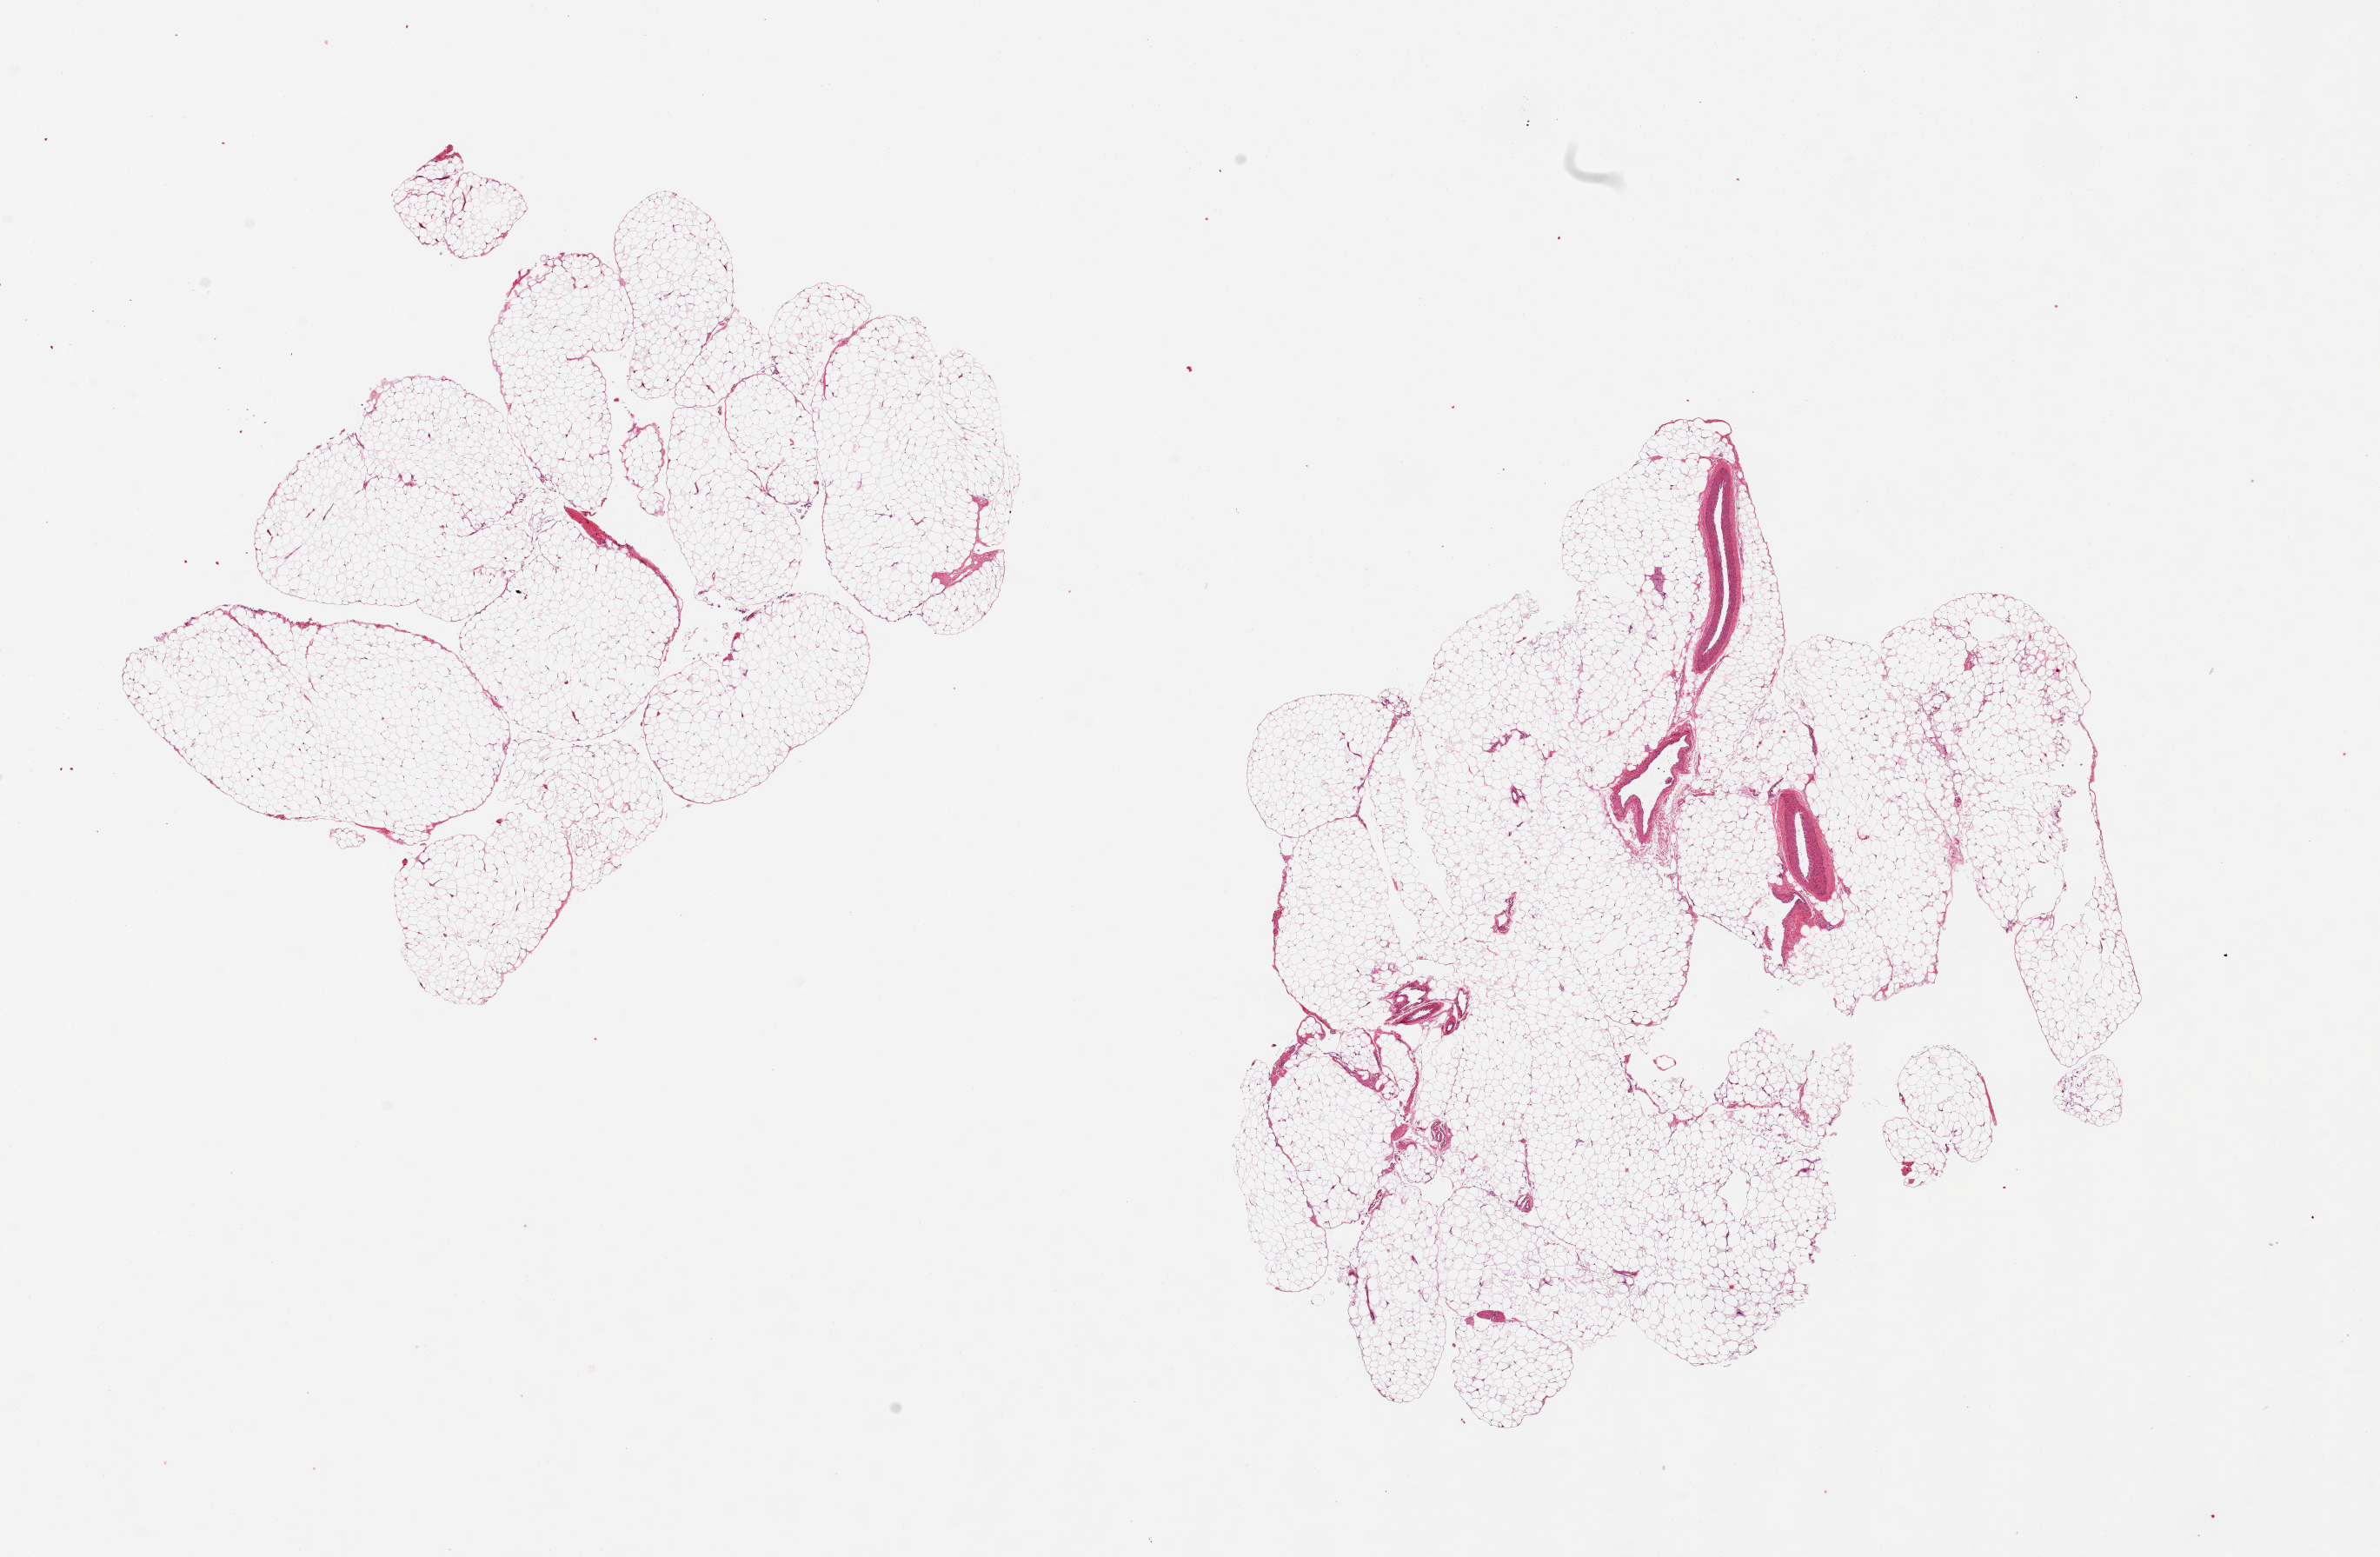
Whole-slide image, H&E stain, brightfield — low-resolution overview of the scanned area, about 21.7 x 14.2 mm (slide scanned at 20x); PAXgene-fixed paraffin-embedded (PFPE) section; sampled site (target tissue): omentum; tissue donor sample.
Review note (as recorded): 2 pieces ~8x5mm, well preserved adipose tissue.